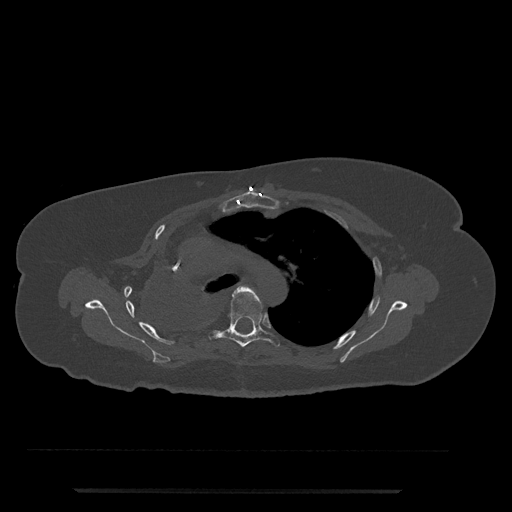
CT including the spine, one axial slice. Position 549 of 797 along the scan axis. Bone window (W 1800 / L 400 HU). 512 × 512 image matrix, field of view 440 × 440 mm. Patient: female, 51 years. From the clinical record (not read from this slice): primary cancer: neuro.
Outlined on this slice (semi-automatically segmented with operator editing):
- T5 vertebra: bounding box [x1, y1, x2, y2] px = [208, 287, 280, 347]